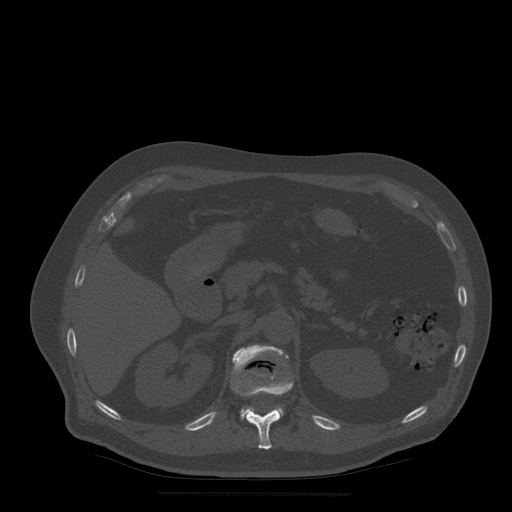
CT including the spine, one axial slice; position 211 of 522 along the scan axis; bone window (W 1800 / L 400 HU); 1.25 mm slice thickness; 512 × 512 image matrix, field of view 420 × 420 mm. Patient age 72 years. Case-level facts recorded for this patient, not image findings: primary cancer: prostate.
Structures marked on this image (semi-automatically segmented with operator editing):
- L1 vertebra: bounding box <233,345,289,420> (left, top, right, bottom; pixels)
- T12 vertebra: <233,376,294,450>